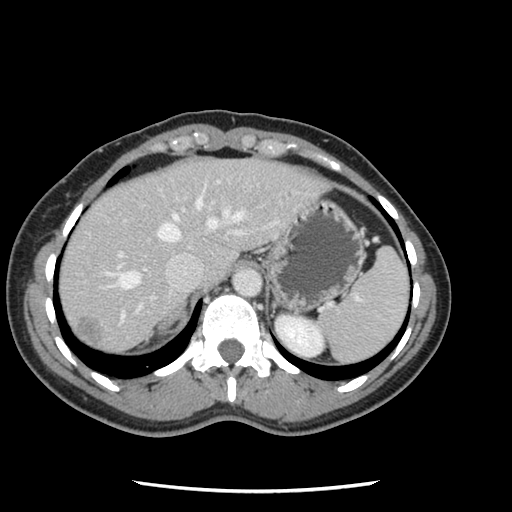
Contrast-enhanced abdominal CT, one axial slice; position 96 of 134 along the scan axis; 120 kVp; soft-tissue window (W 400 / L 40 HU); 2.5 mm slice thickness; 512 × 512 image matrix, field of view 330 × 330 mm. Female patient, age 43 years. From the clinical record (not read from this slice): diagnosis: colorectal cancer liver metastases, imaged before liver resection; multiple liver metastases: yes; largest metastasis: 3.4 cm; chemotherapy before resection: no.
Structures marked on this image (manually delineated by an expert):
- hepatic veins: bounding box (x1, y1, x2, y2) in pixels: (107, 199, 245, 319)
- liver: (60, 159, 323, 354)
- planned liver remnant (the part of the liver to remain after resection): (60, 167, 194, 308)
- portal vein (with intrahepatic branches): (117, 181, 276, 314)
- liver metastasis: (74, 318, 103, 349)